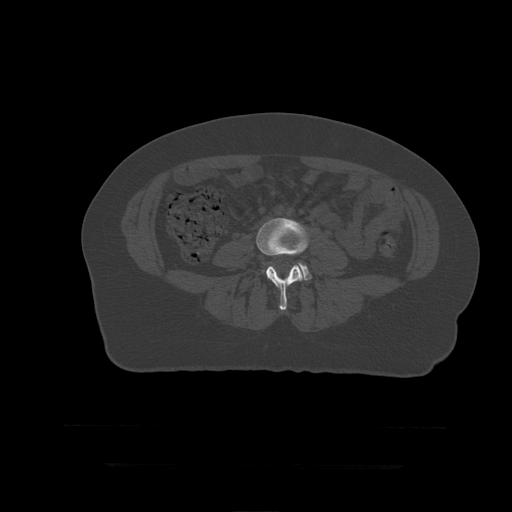
CT including the spine, one axial slice. Position 90 of 399 along the scan axis. Bone window (W 1800 / L 400 HU). 1.25 mm slice thickness. 512 × 512 image matrix, field of view 450 × 450 mm. Patient age 41 years. Case-level facts recorded for this patient, not image findings: primary cancer: breast.
Outlined on this slice (semi-automatically segmented with operator editing):
- L4 vertebra: bounding box (x1, y1, x2, y2) in pixels: (257, 218, 309, 310)
- L5 vertebra: (263, 262, 312, 281)